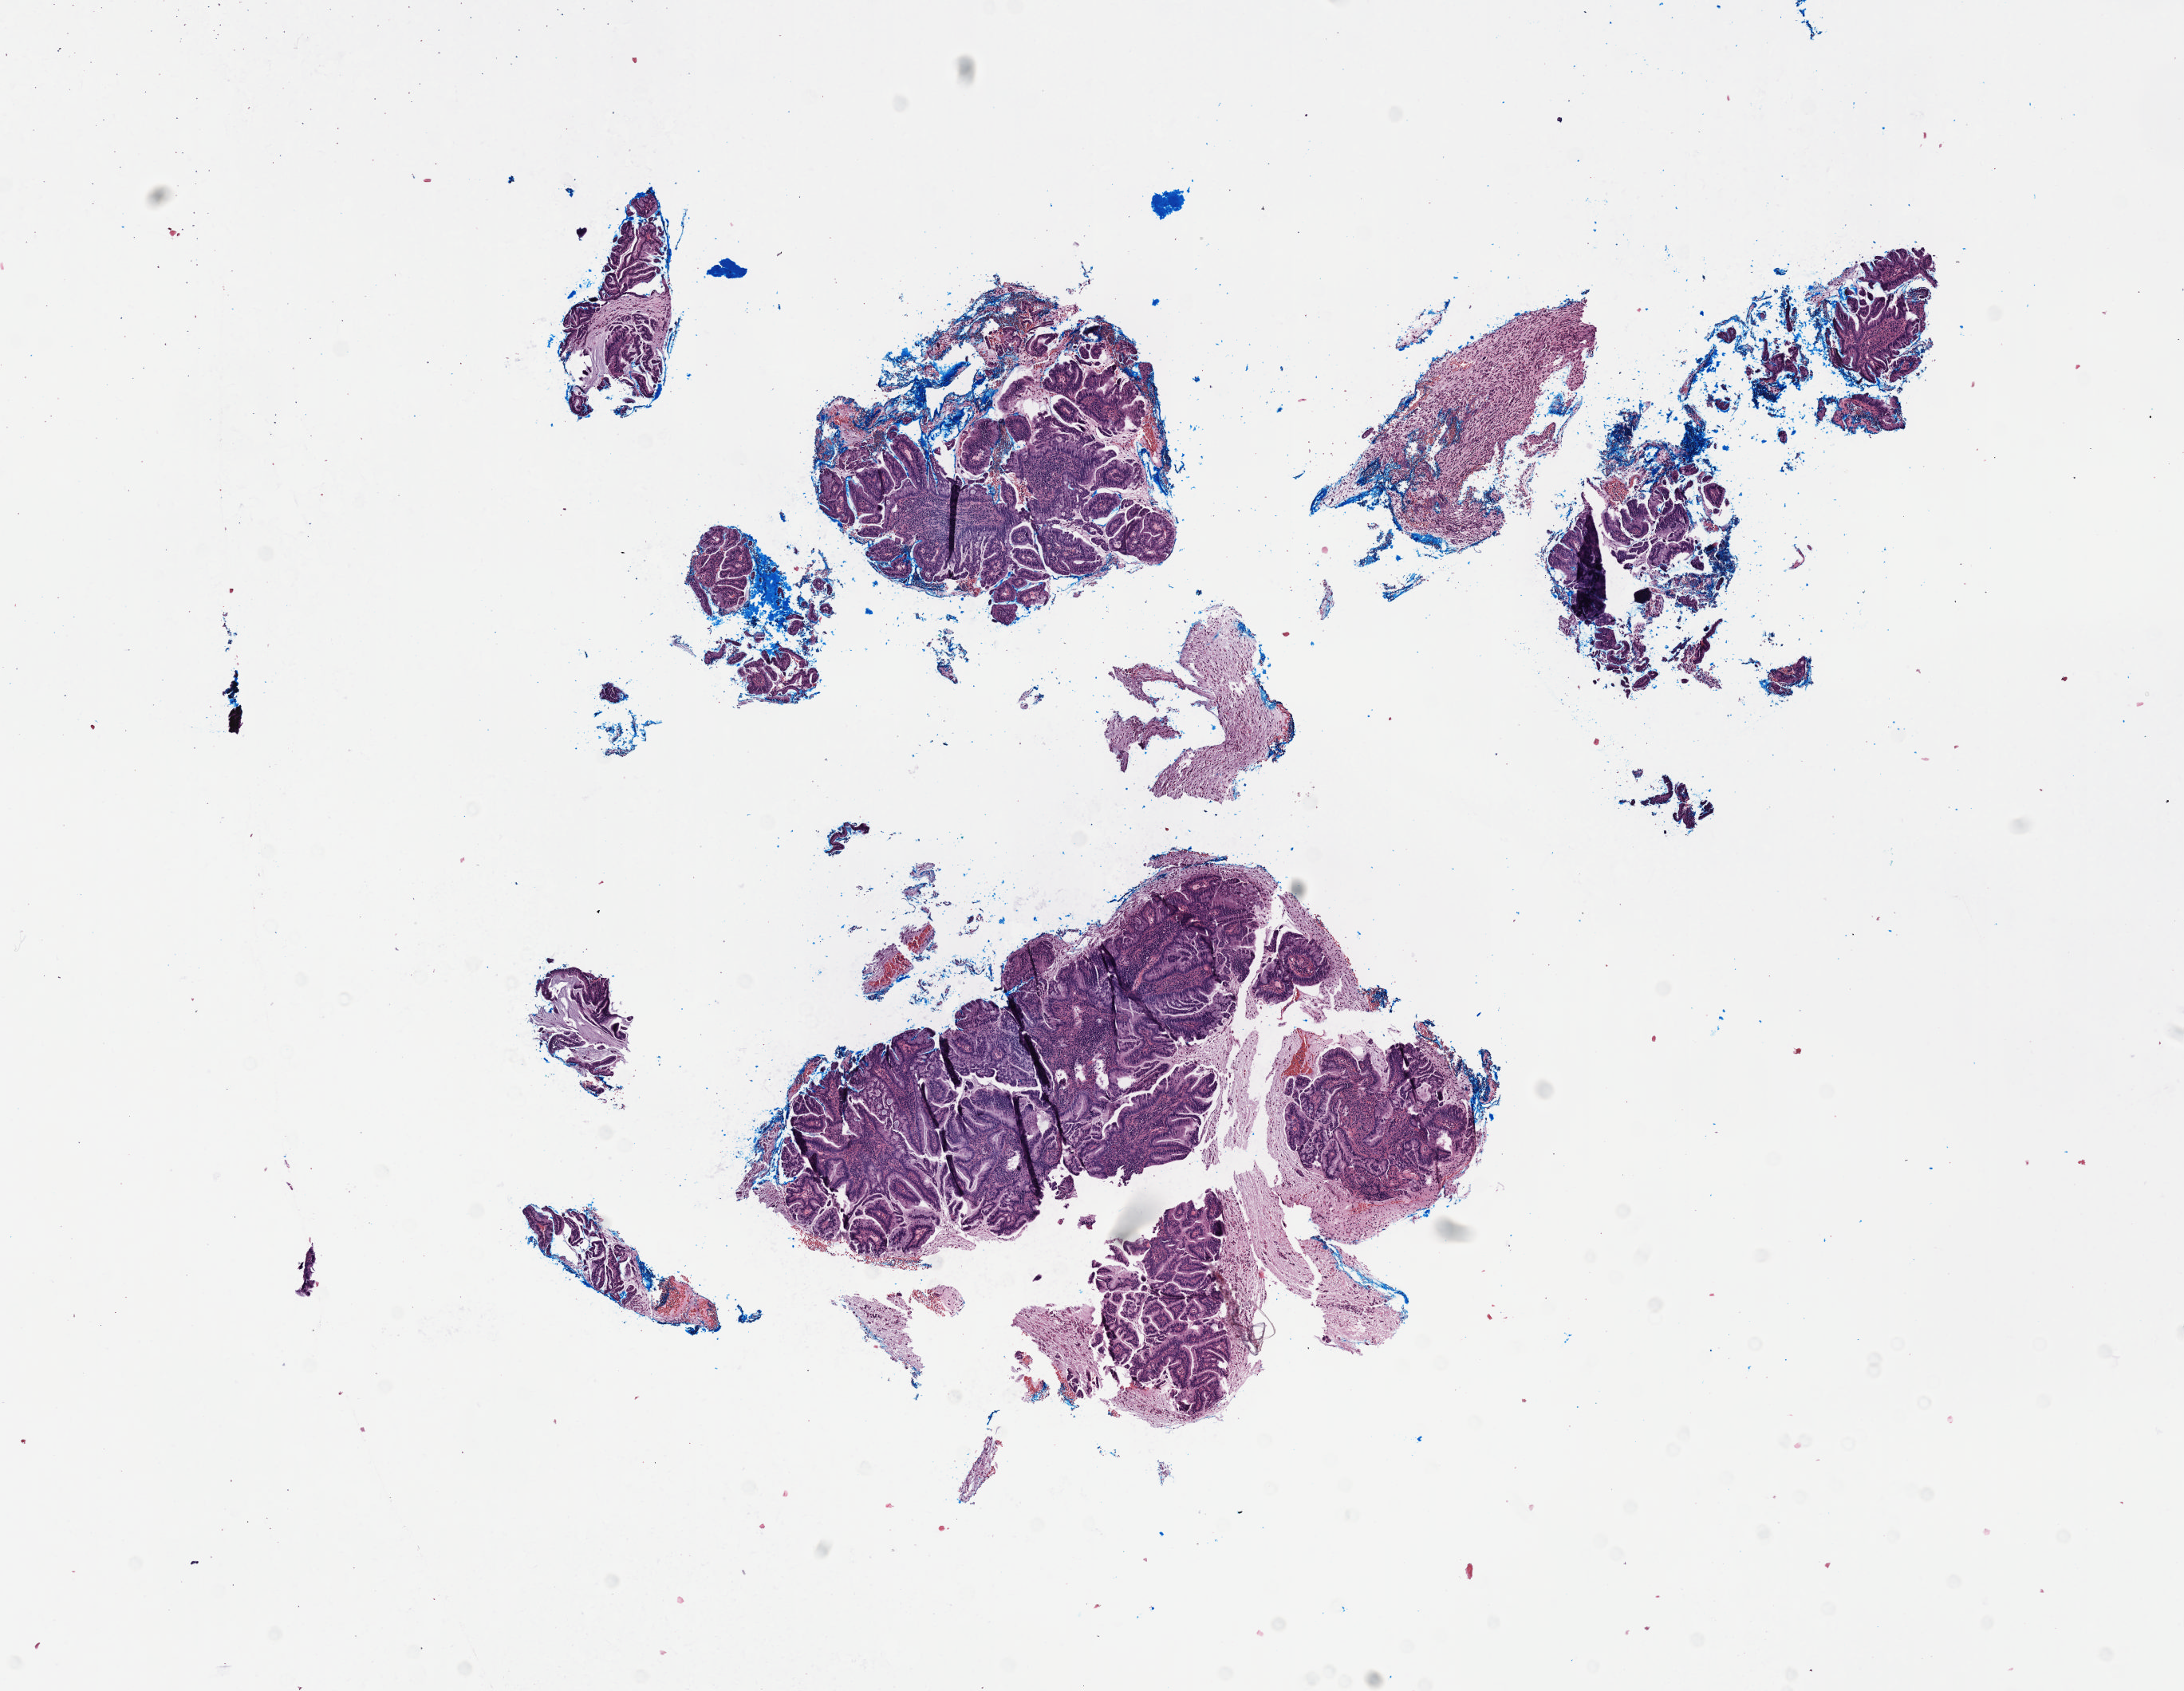
Whole-slide histology image, Hematoxylin and eosin (H&E) stained — whole scanned area (about 11.1 x 8.6 mm, from a 40x scan) shown as a low-resolution overview, formalin-fixed paraffin-embedded (FFPE) diagnostic section, primary tumour sample from the cervix. Female, age 46 years at initial diagnosis. Histologic grade: G2 (moderately differentiated).
Diagnosis: Mucinous adenocarcinoma, endocervical type (cervix uteri). FIGO stage: IVB.